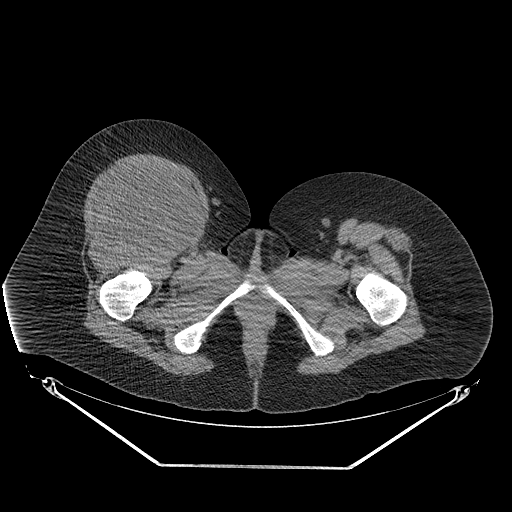
CT of an extremity soft-tissue mass (from a PET/CT study), one axial slice. Soft-tissue window (W 400 / L 40 HU). 3.75 mm slice thickness. 512 × 512 image matrix. Female patient. Case-level facts recorded for this patient, not image findings: histological type: malignant solitary fibrous tumor; grade: intermediate; site of the primary tumour: right thigh.
Annotated regions visible in this slice (expert contour drawn on MRI and transferred to this co-registered scan by the dataset authors):
- gross tumour volume including surrounding oedema: bounding box <85,162,195,241> (left, top, right, bottom; pixels)
- gross tumour volume (mass): <85,164,193,241>